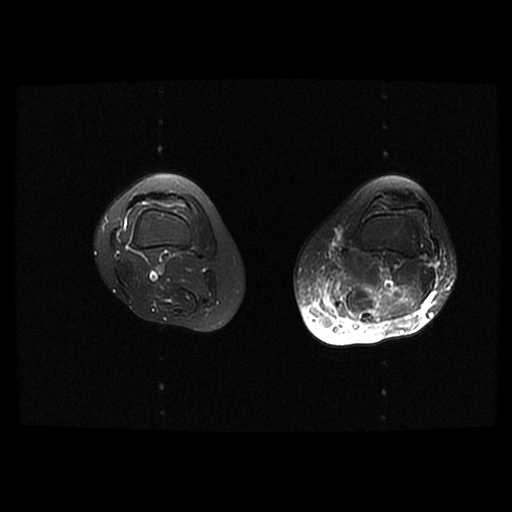
MRI of an extremity soft-tissue mass, one axial slice. Position 13 of 42 along the scan axis. T2-weighted fat-saturated. 512 × 512 image matrix, field of view 420 × 420 mm. Female patient. From the clinical record (not read from this slice): histological type: pleomorphic leiomyosarcoma; grade: high; site of the primary tumour: left thigh.
Outlined on this slice (outlined manually by an expert reader):
- gross tumour volume including surrounding oedema: bounding box (x1, y1, x2, y2) in pixels: (317, 267, 344, 317)